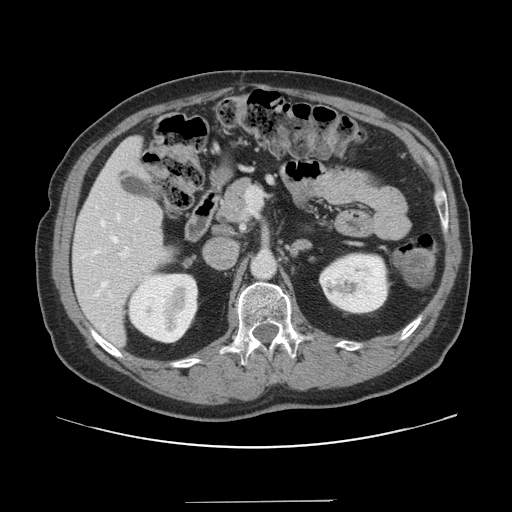
Contrast-enhanced abdominal CT, one axial slice. Position 75 of 151 along the scan axis. Intravenous contrast given. Soft-tissue window (W 400 / L 40 HU). 2.5 mm slice thickness. 512 × 512 image matrix, field of view 399 × 399 mm. Male patient, age 63 years. From the clinical record (not read from this slice): diagnosis: colorectal cancer liver metastases, imaged before liver resection; multiple liver metastases: no; largest metastasis: 2.1 cm; chemotherapy before resection: no.
Structures marked on this image (manually delineated by an expert):
- hepatic veins: bounding box <101,214,120,287> (left, top, right, bottom; pixels)
- liver: <73,138,171,347>
- planned liver remnant (the part of the liver to remain after resection): <74,138,171,346>
- portal vein (with intrahepatic branches): <119,189,261,258>